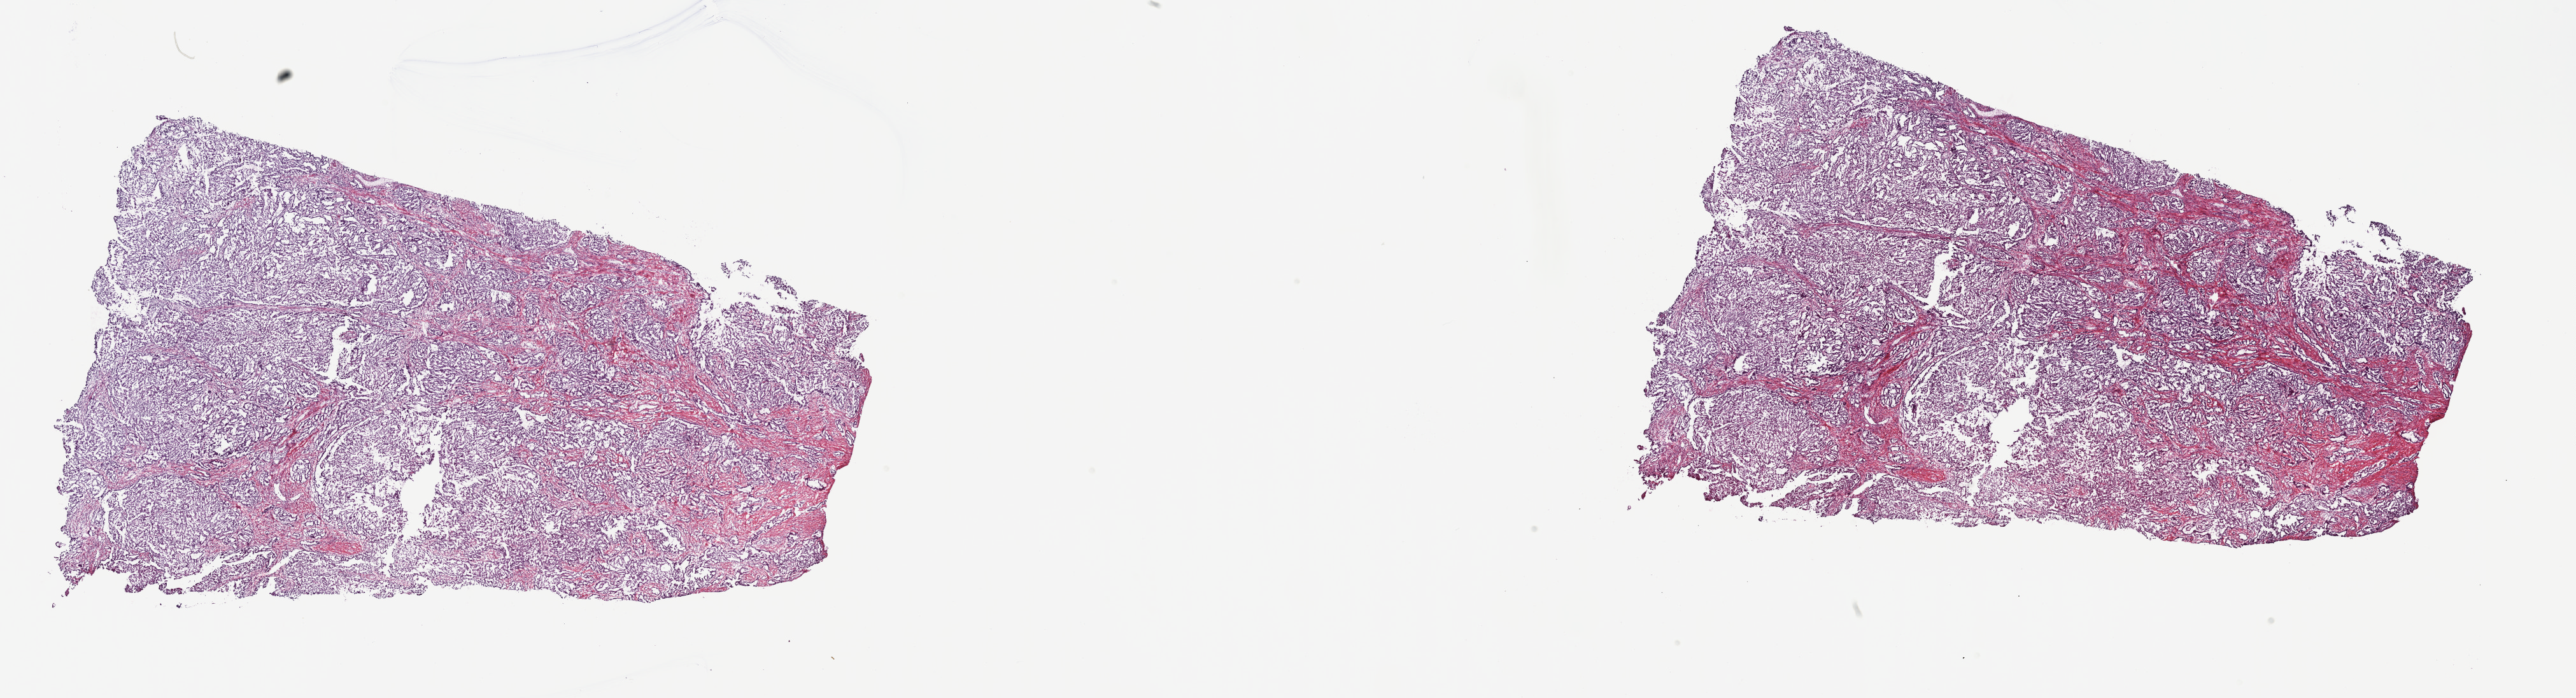
Hematoxylin and eosin (H&E) stained whole-slide image — low-resolution overview of the scanned area, about 32.7 x 8.9 mm (acquisition: 40x scan), frozen section from the top of the tissue portion, primary tumour sample from the mesothelium. Male, age 56 years at initial diagnosis. Composition of this section per pathologist review: tumour cells 100%, tumour nuclei 75%, normal cells 0%, stromal cells 0%, necrosis 0%. Infiltration values recorded for this section: lymphocyte infiltration 2%, monocyte infiltration 0%, neutrophil infiltration 0%.
AJCC pathologic stage: IV (6th edition). TNM: T4 N0 MX. Histologic diagnosis: Epithelioid mesothelioma, malignant.